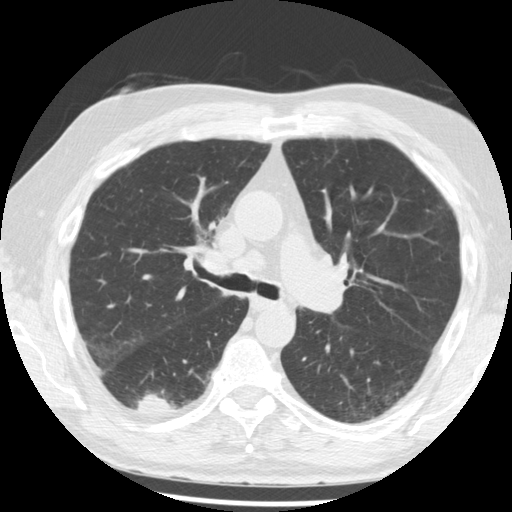
Low-dose screening chest CT, one axial slice. Slice 132 of 221 in the series (ordered by position). Reconstruction kernel STANDARD. 120 kVp. Lung window (W 1500 / L -600 HU). 512 × 512 image matrix, field of view 350 × 350 mm.
Structures marked on this image (manually delineated by an expert):
- lesion 1 (tumor, lower lobe of right lung): bounding box <137,391,176,413> (left, top, right, bottom; pixels)